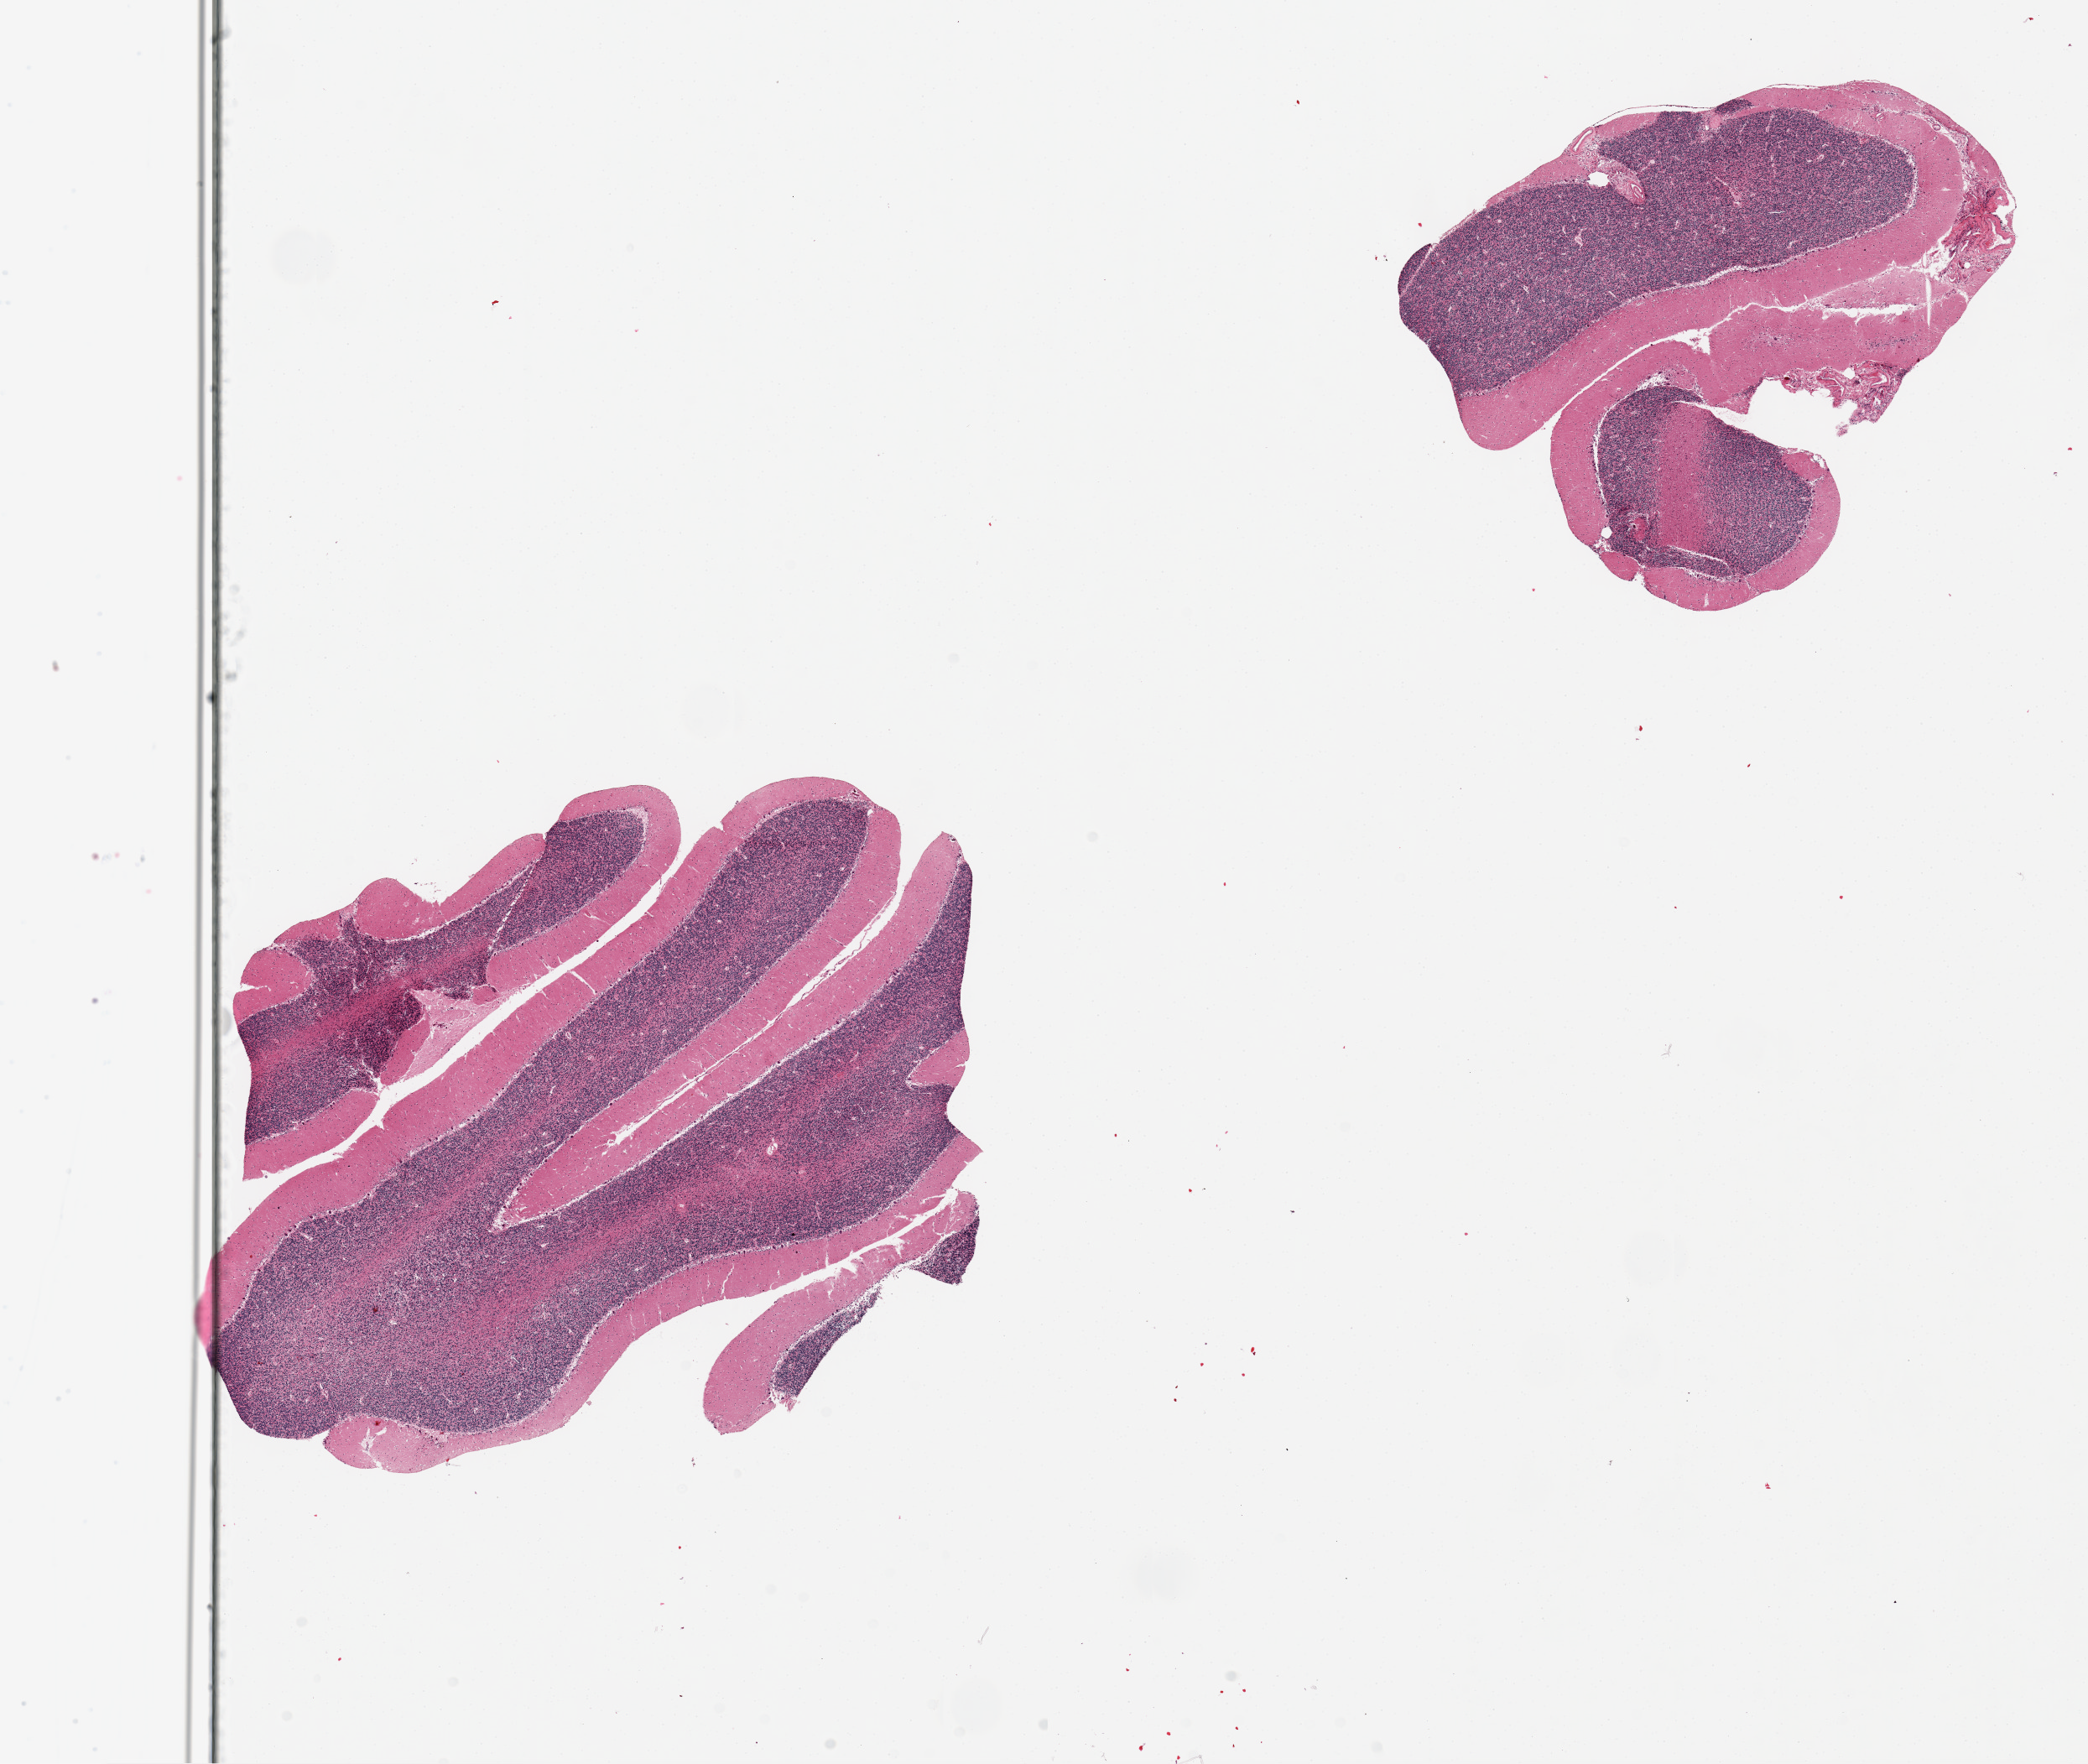
Whole-slide image, haematoxylin and eosin stain — whole scanned area (about 19.7 x 16.6 mm, acquisition: 20x scan) shown as a low-resolution overview, PAXgene-fixed paraffin-embedded (PFPE) section, target tissue: cerebellum, donor tissue sample. Donor sex: male.
Reviewer comment on this tissue sample: 2 pieces; Some-- but not all -- Purkinje cells show nuclear loss c/w hypoxia antemortem.